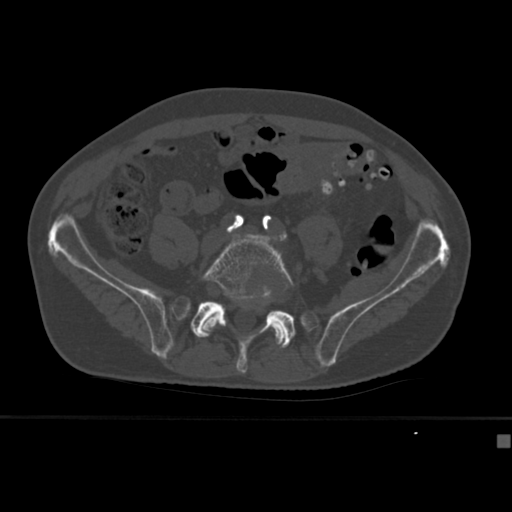
CT including the spine, one axial slice; position 81 of 430 along the scan axis; reconstruction kernel Br40s; 120 kVp; bone window (W 1800 / L 400 HU); 1.5 mm slice thickness; 512 × 512 image matrix, field of view 337 × 337 mm. Male patient, age 64 years. Case-level facts recorded for this patient, not image findings: primary cancer: uterus.
Annotated regions visible in this slice (semi-automatic segmentation, software-assisted and operator-edited):
- L5 vertebra: box from (x=196, y=233) to (x=294, y=349) px